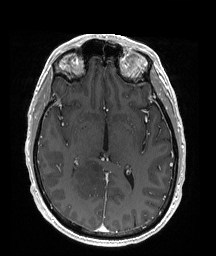
Brain MRI from a brain-tumour surgery series, one axial slice. Position 99 of 176 along the scan axis. T1-weighted post-contrast. 216 × 256 image matrix. Case-level facts recorded for this patient, not image findings: histopathology: Oligodendroglioma; WHO grade: 2; IDH mutation: yes; tumour location: Right Parietal.
Outlined on this slice (expert manual segmentation):
- tumour: bounding box [x1, y1, x2, y2] px = [70, 156, 111, 194]